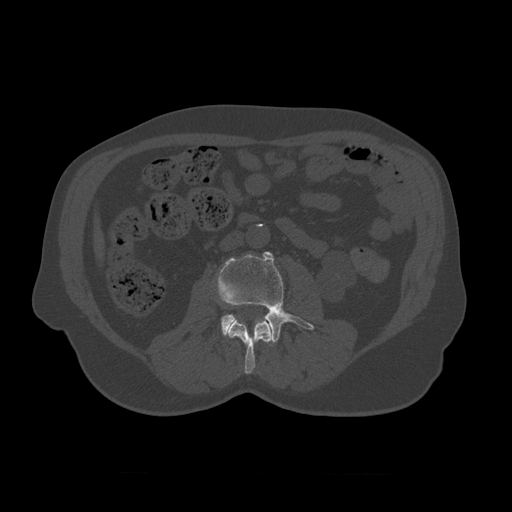
CT including the spine, one axial slice; slice 315 of 450 in the series (ordered by position); 120 kVp; bone window (W 1800 / L 400 HU); 1.25 mm slice thickness; 512 × 512 image matrix. Patient age 75 years. From the clinical record (not read from this slice): primary cancer: prostate.
Outlined on this slice (semi-automatic segmentation, software-assisted and operator-edited):
- L2 vertebra: bounding box (x1, y1, x2, y2) in pixels: (227, 315, 273, 374)
- L3 vertebra: (216, 251, 315, 347)